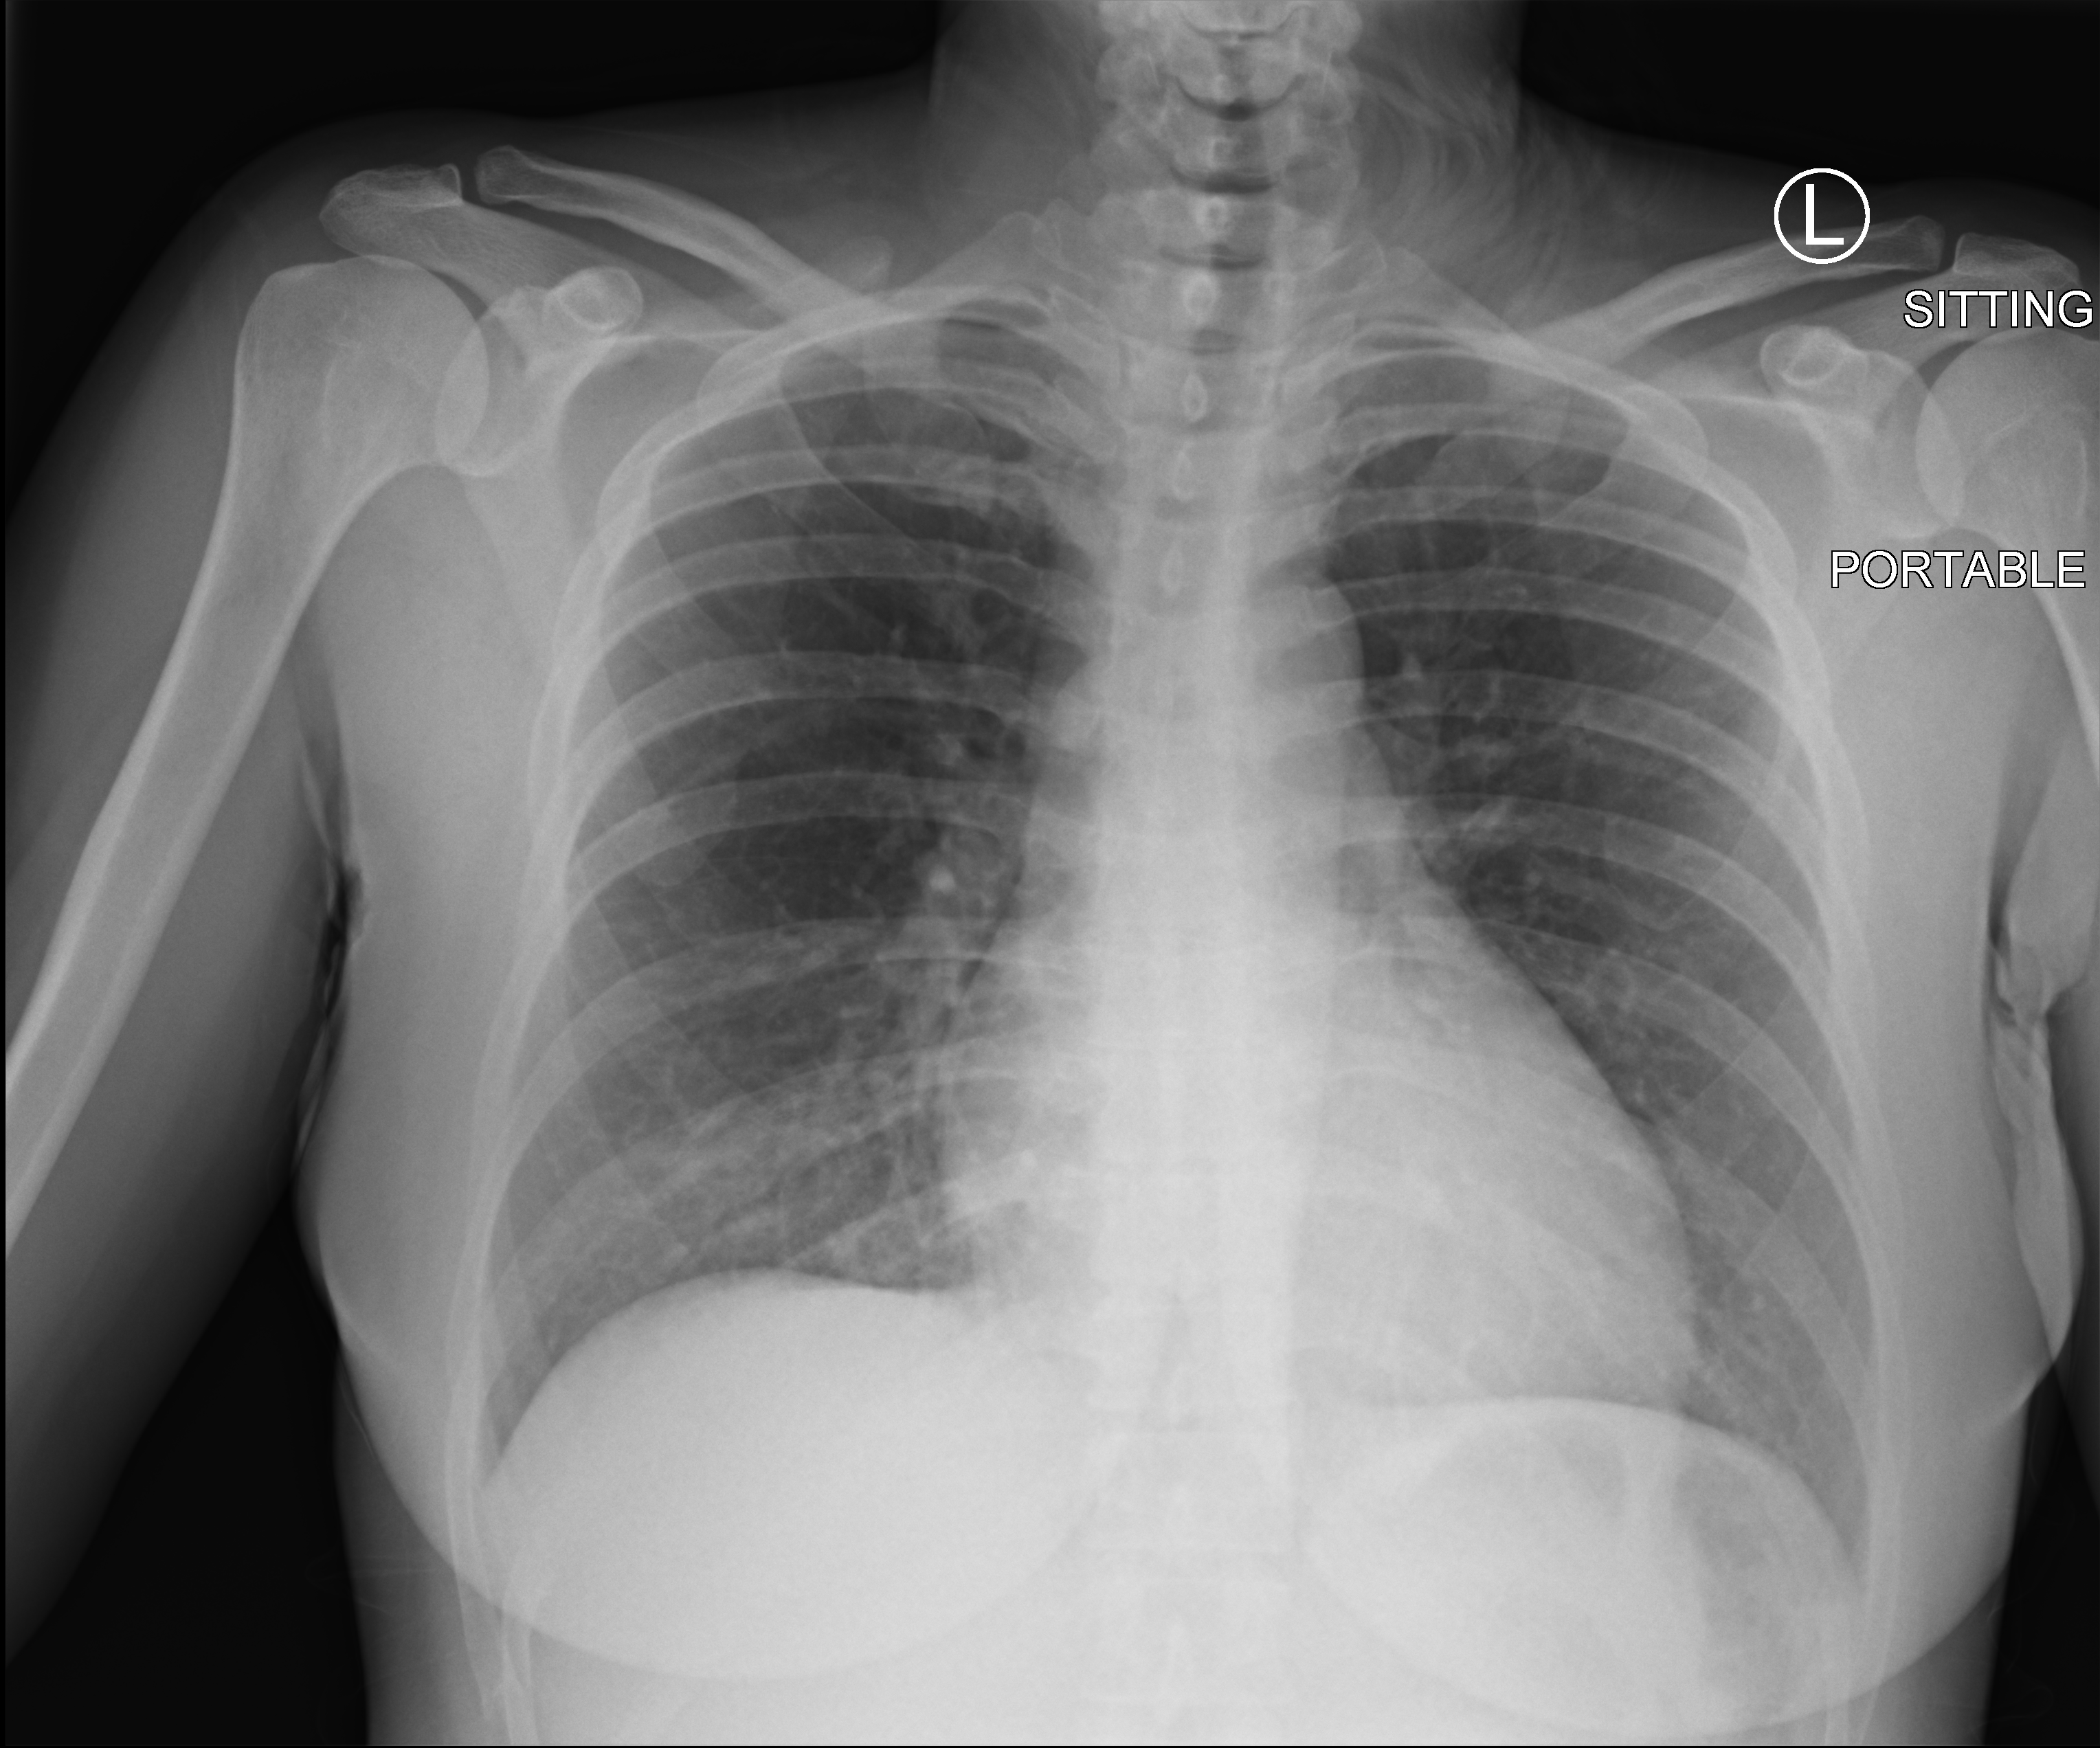
Bedside chest radiograph (computed radiography), anteroposterior (AP) projection. Patient hospitalised with COVID-19; female, aged 18–59 years.
Hospital-stay facts (about this admission, not read from this image; timing relative to this image not recorded): admitted to intensive care during this hospital stay: no; length of hospital stay: 1 day; smoking status (admission record): never.